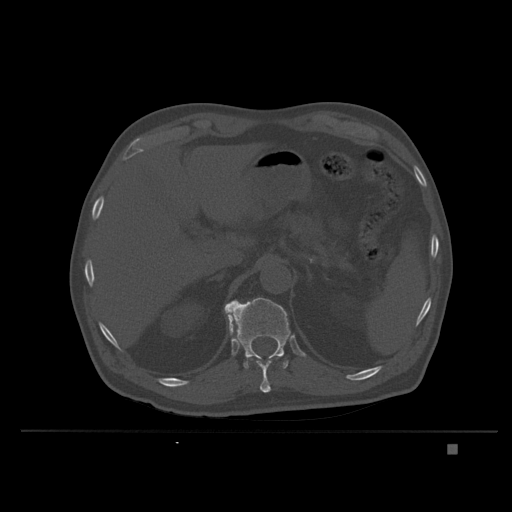
CT including the spine, one axial slice. Slice 165 of 435 in the series (ordered by position). Bone window (W 1800 / L 400 HU). 1.5 mm slice thickness. 512 × 512 image matrix, field of view 434 × 434 mm. Male patient, age 73 years. From the clinical record (not read from this slice): primary cancer: skin.
Structures marked on this image (semi-automatically segmented with operator editing):
- T11 vertebra: box from (x=230, y=325) to (x=272, y=393) px
- T12 vertebra: (x=224, y=297)–(x=291, y=369)